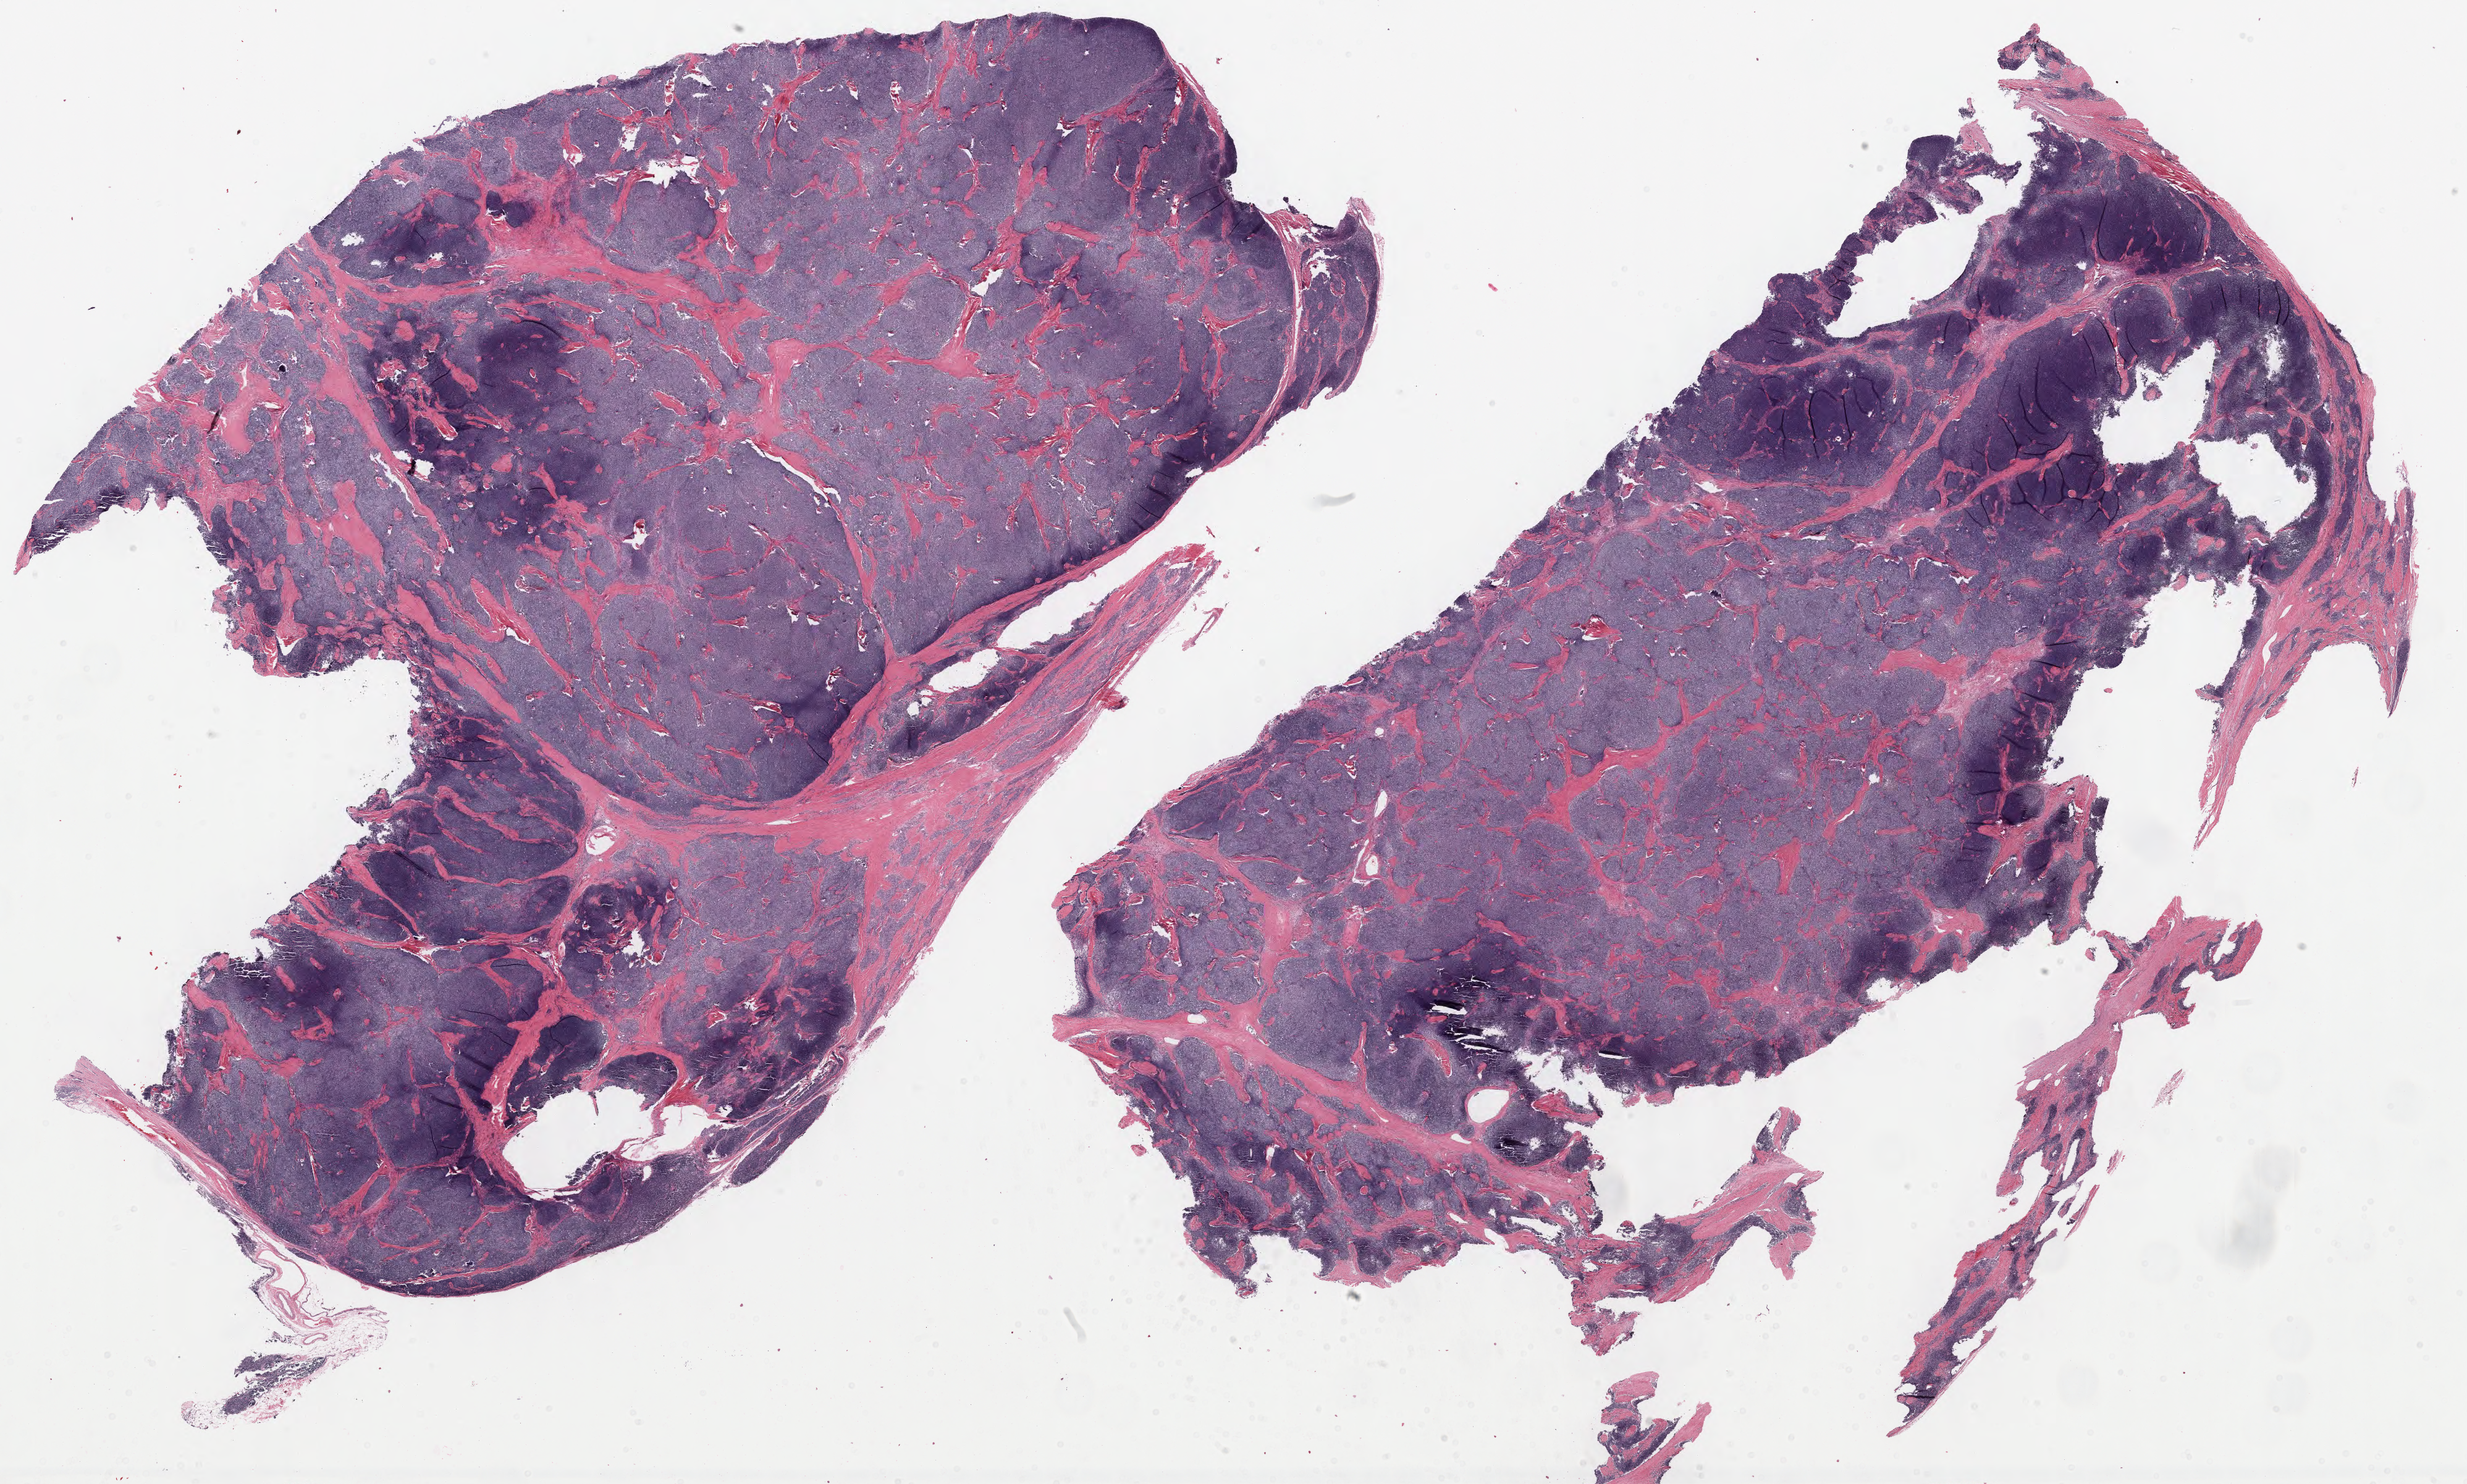
Digitized Hematoxylin and eosin (H&E) stained tissue section (whole slide) — whole scanned area (about 31.7 x 19.0 mm, acquisition: 40x scan) shown as a low-resolution overview; formalin-fixed paraffin-embedded (FFPE) diagnostic section; sample: primary tumour, thymus. Female patient; age at initial diagnosis 50 years.
* pathologic diagnosis: Thymoma, type AB, malignant